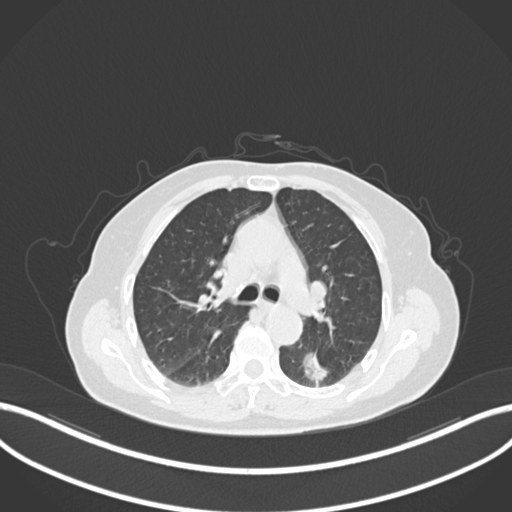
Chest CT, one axial slice; slice 538 of 727 in the series (ordered by position); reconstruction kernel B30f; lung window (W 1500 / L -600 HU); 1 mm slice thickness; 512 × 512 image matrix, field of view 400 × 400 mm. Patient: female, 70 years. From the clinical record (not read from this slice): clinical TNM (as recorded): T1c N0 M0.
Annotated regions visible in this slice (rectangle marked by the reading radiologist):
- lung tumour (recorded histology: adenocarcinoma): bounding box <301,348,334,385> (left, top, right, bottom; pixels)